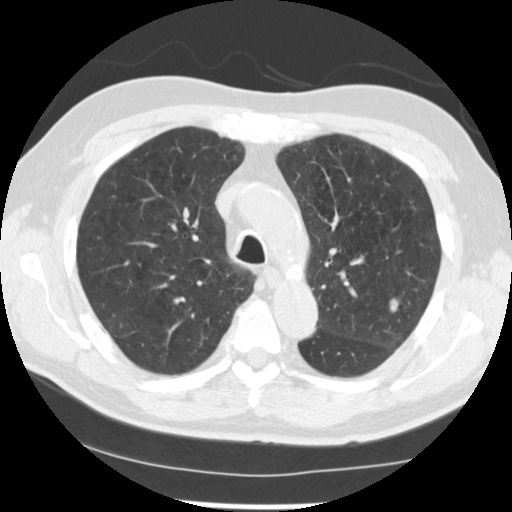
Low-dose screening chest CT, one axial slice. Slice 177 of 249 in the series (ordered by position). Lung window (W 1500 / L -600 HU). 2.5 mm slice thickness. 512 × 512 image matrix, field of view 341 × 341 mm.
Structures marked on this image (expert manual segmentation):
- lesion 1 (tumor, upper lobe of left lung): bounding box (x1, y1, x2, y2) in pixels: (390, 299, 399, 311)